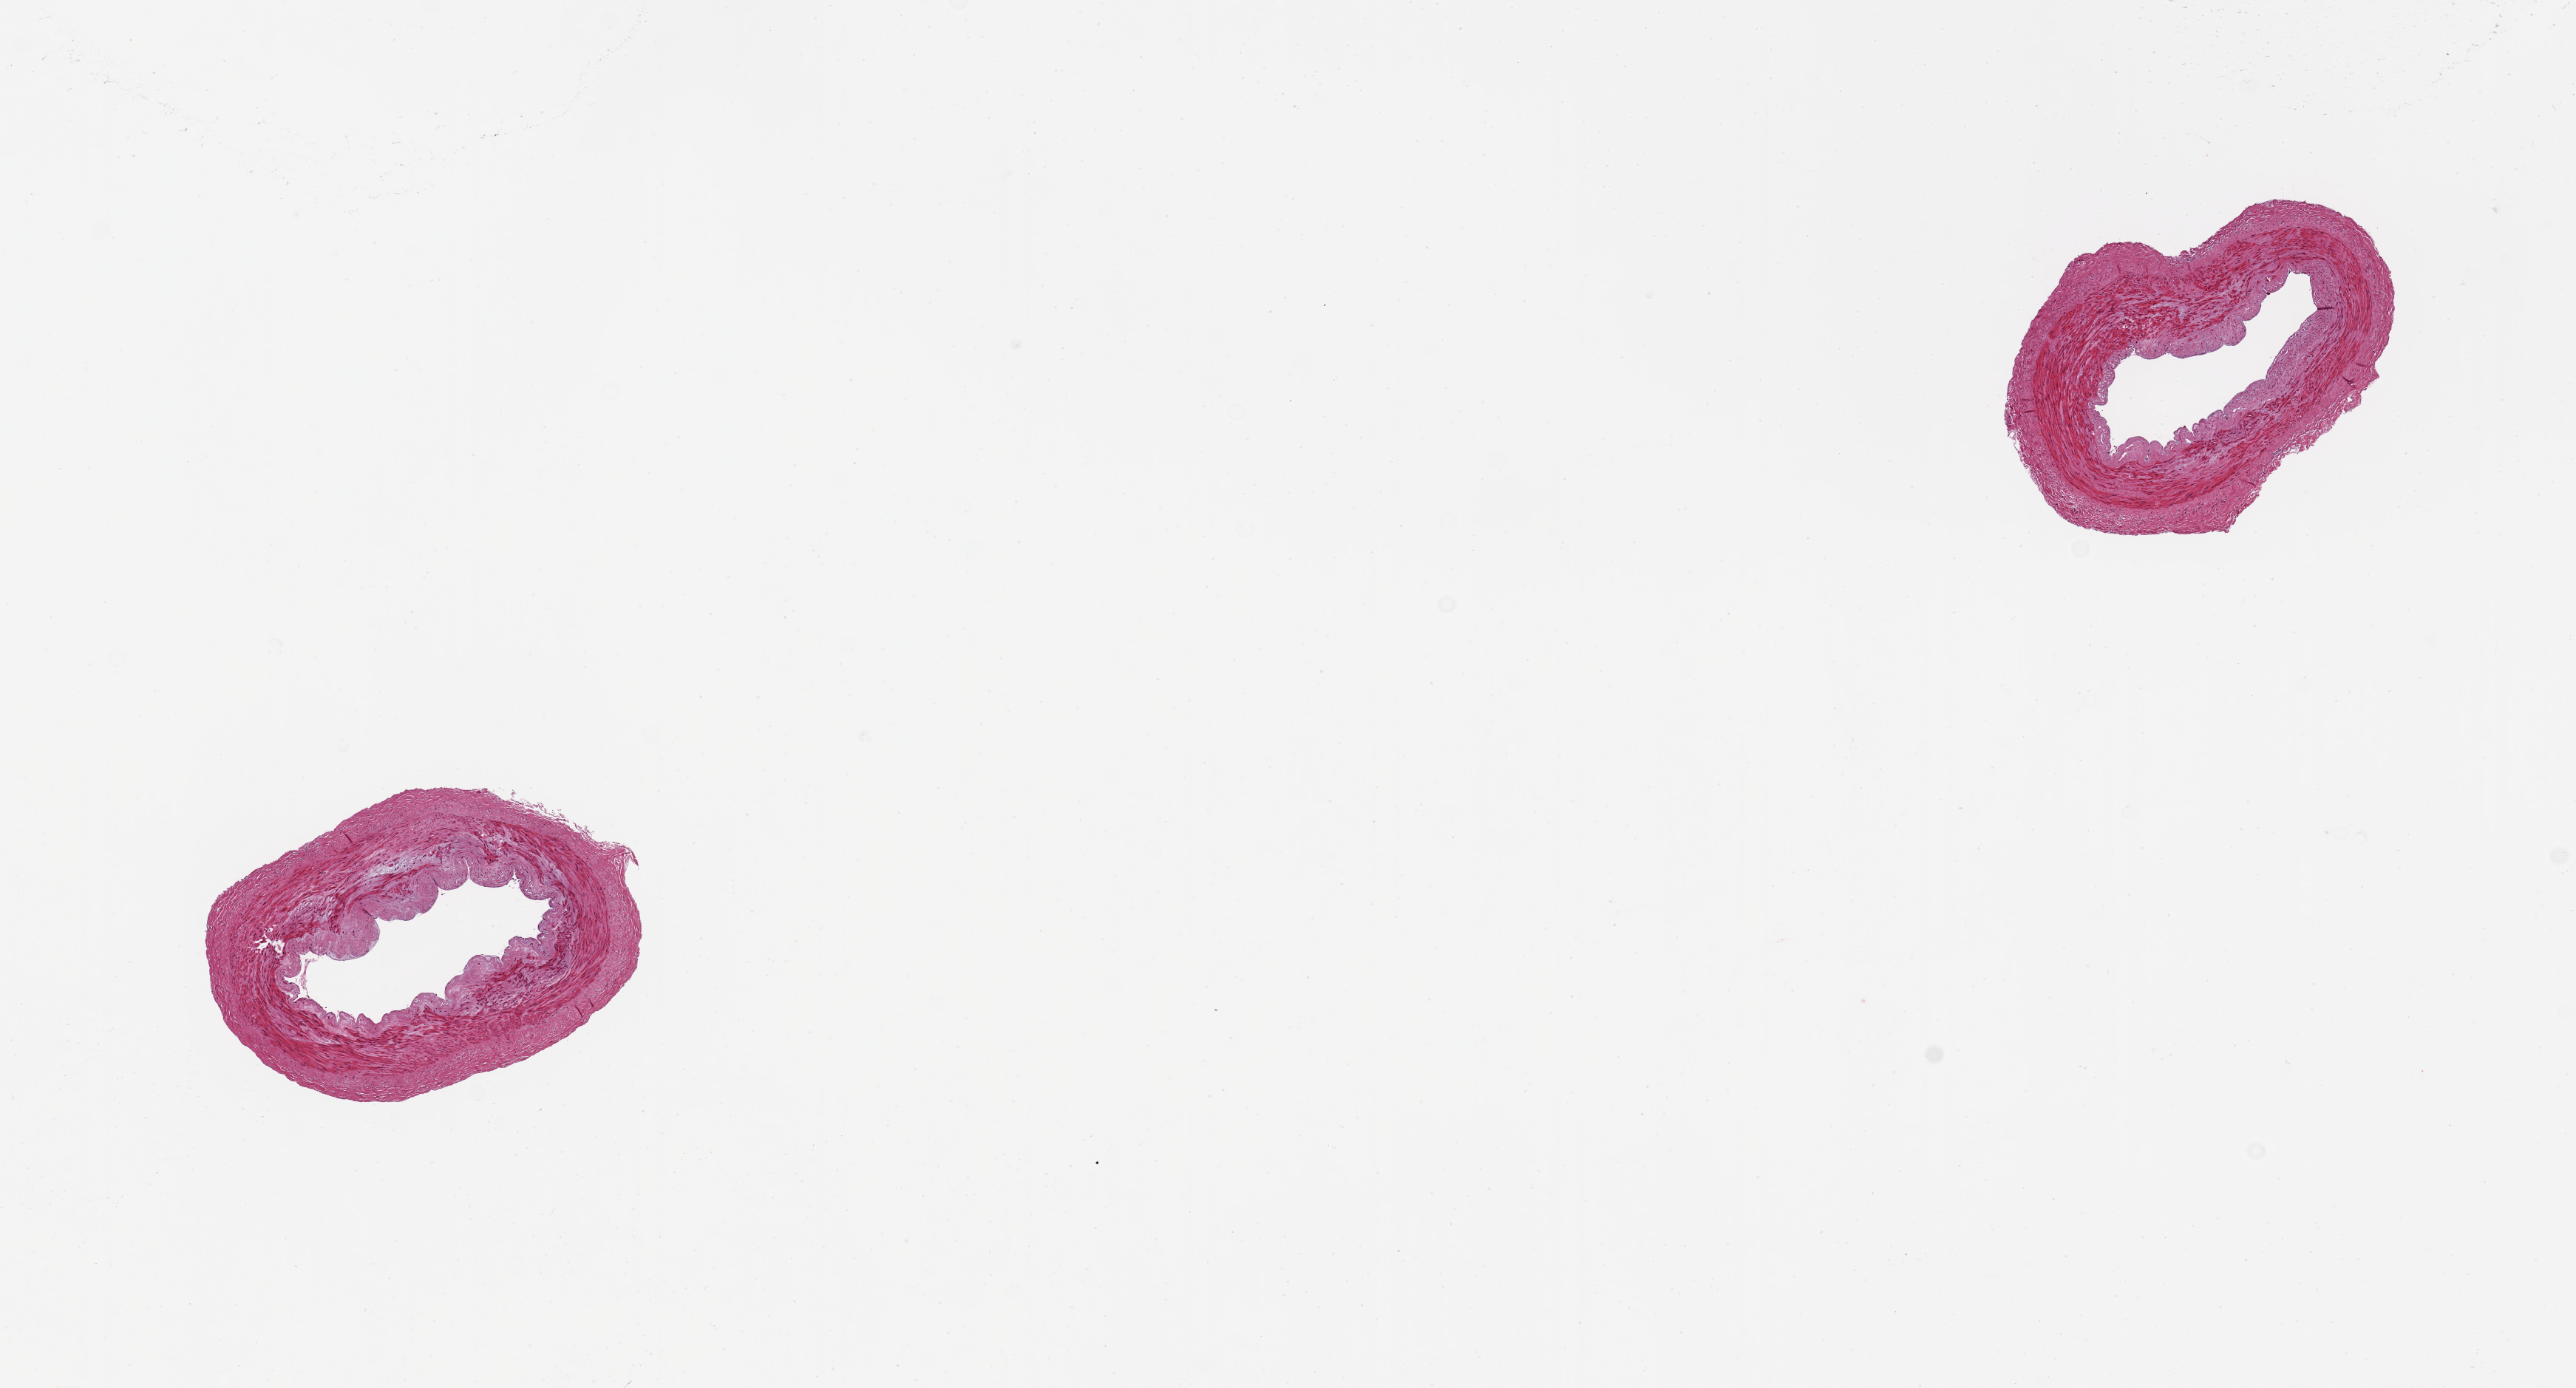
Hematoxylin and eosin (H&E) whole-slide image, a low-resolution overview of the entire scanned area, about 13.8 x 7.4 mm (slide scanned at 20x); PAXgene-fixed paraffin-embedded (PFPE) section; sampled site (target tissue): tibial artery; tissue donor sample.
Review note (as recorded): 2 pieces of 2 muscular arteries ; slight intimal thickening. Focal atherosis.